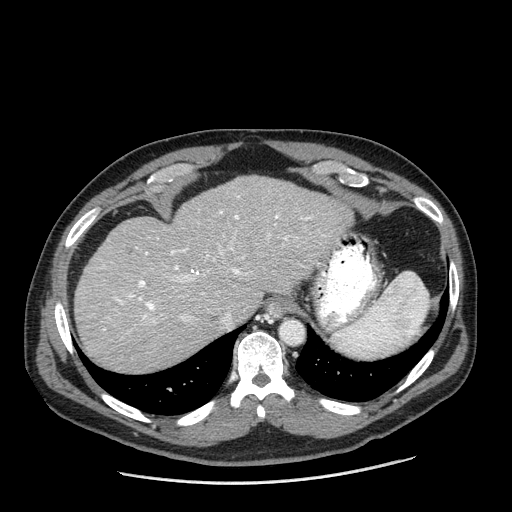
Contrast-enhanced abdominal CT (liver protocol), one axial slice. Slice 147 of 198 in the series (ordered by position). Reconstruction kernel STANDARD. One of 2 acquisitions stored at this slice position. Soft-tissue window (W 400 / L 40 HU). 512 × 512 image matrix, field of view 400 × 400 mm. From the clinical record (not read from this slice): diagnosis: hepatocellular carcinoma (patient treated with transarterial chemoembolisation; whether this scan precedes or follows treatment is not stated here); TNM stage (as recorded): Stage-II; Child-Pugh class: A.
Structures marked on this image (semi-automatic segmentation, software-assisted and operator-edited):
- liver parenchyma outside the tumour (the mass and vessels are separate outlines, so this box may not span the whole liver): bounding box (x1, y1, x2, y2) in pixels: (74, 176, 352, 372)
- liver vessels: (103, 196, 325, 330)